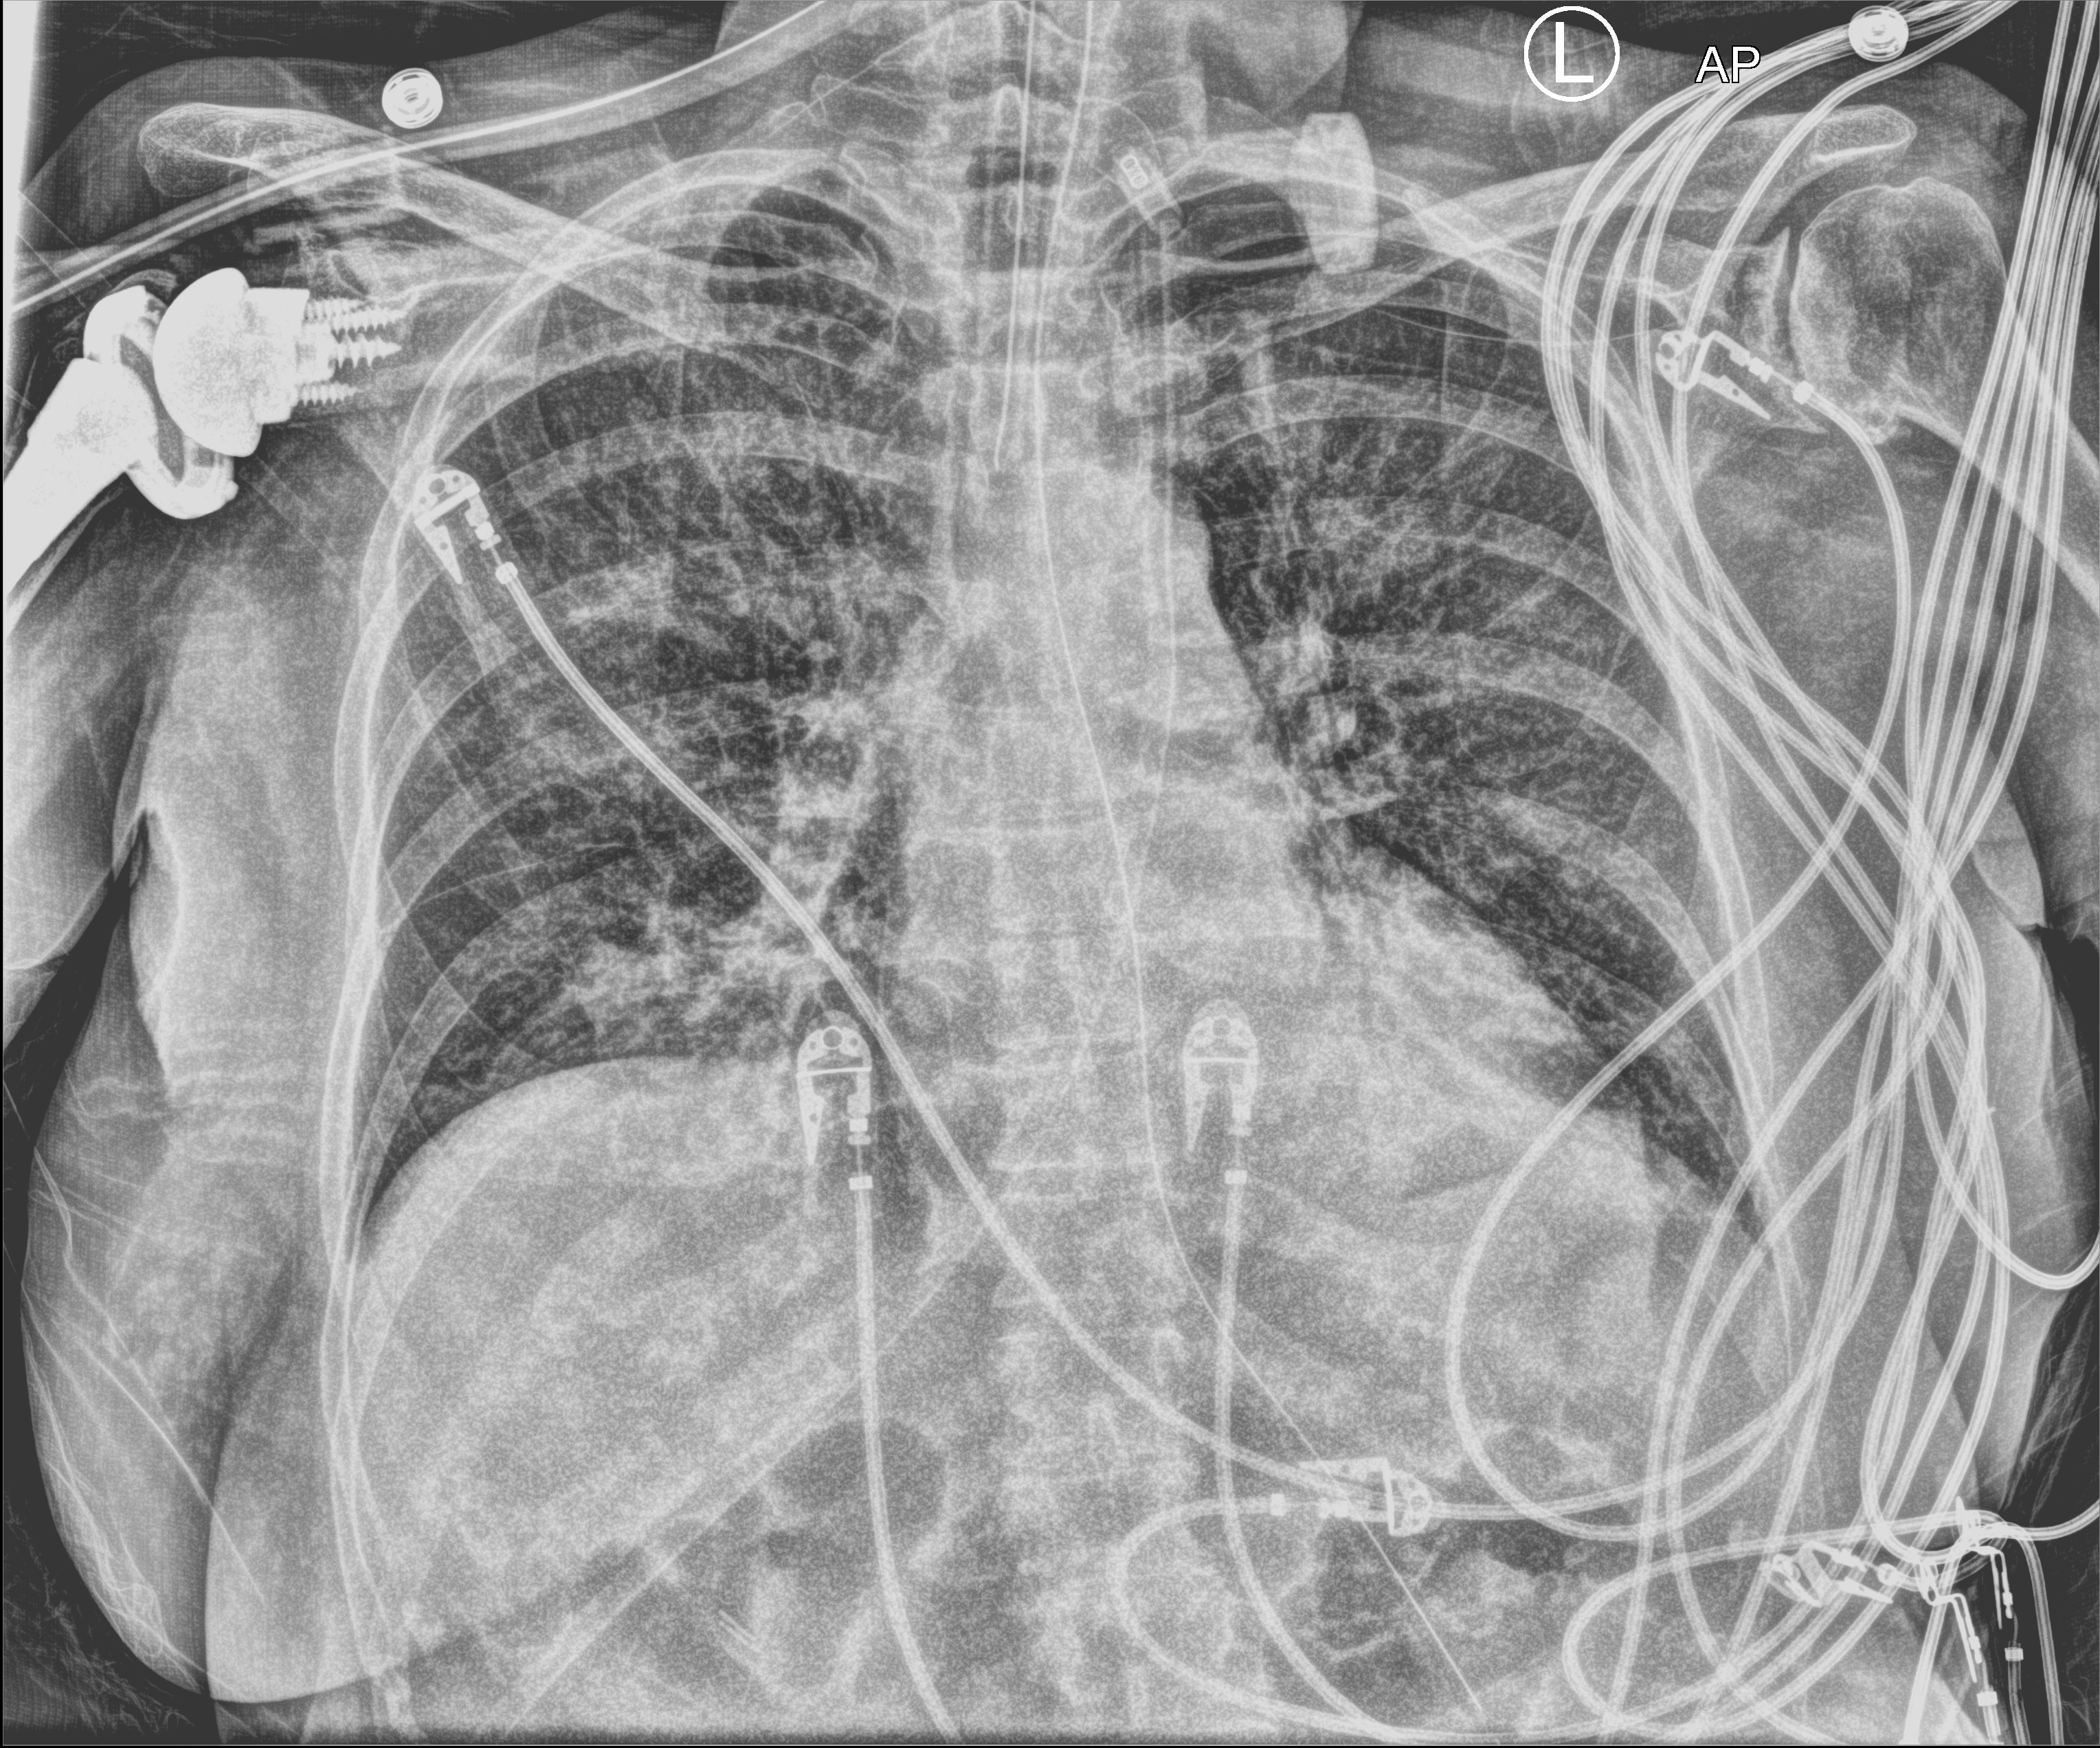
Bedside chest radiograph (computed radiography); anteroposterior (AP) projection. Patient hospitalised with COVID-19; female, aged 60–74 years.
Hospital-stay facts (about this admission, not read from this image; timing relative to this image not recorded): admitted to intensive care during this hospital stay: yes; length of hospital stay: 27 days; mechanically ventilated during this hospital stay: yes.